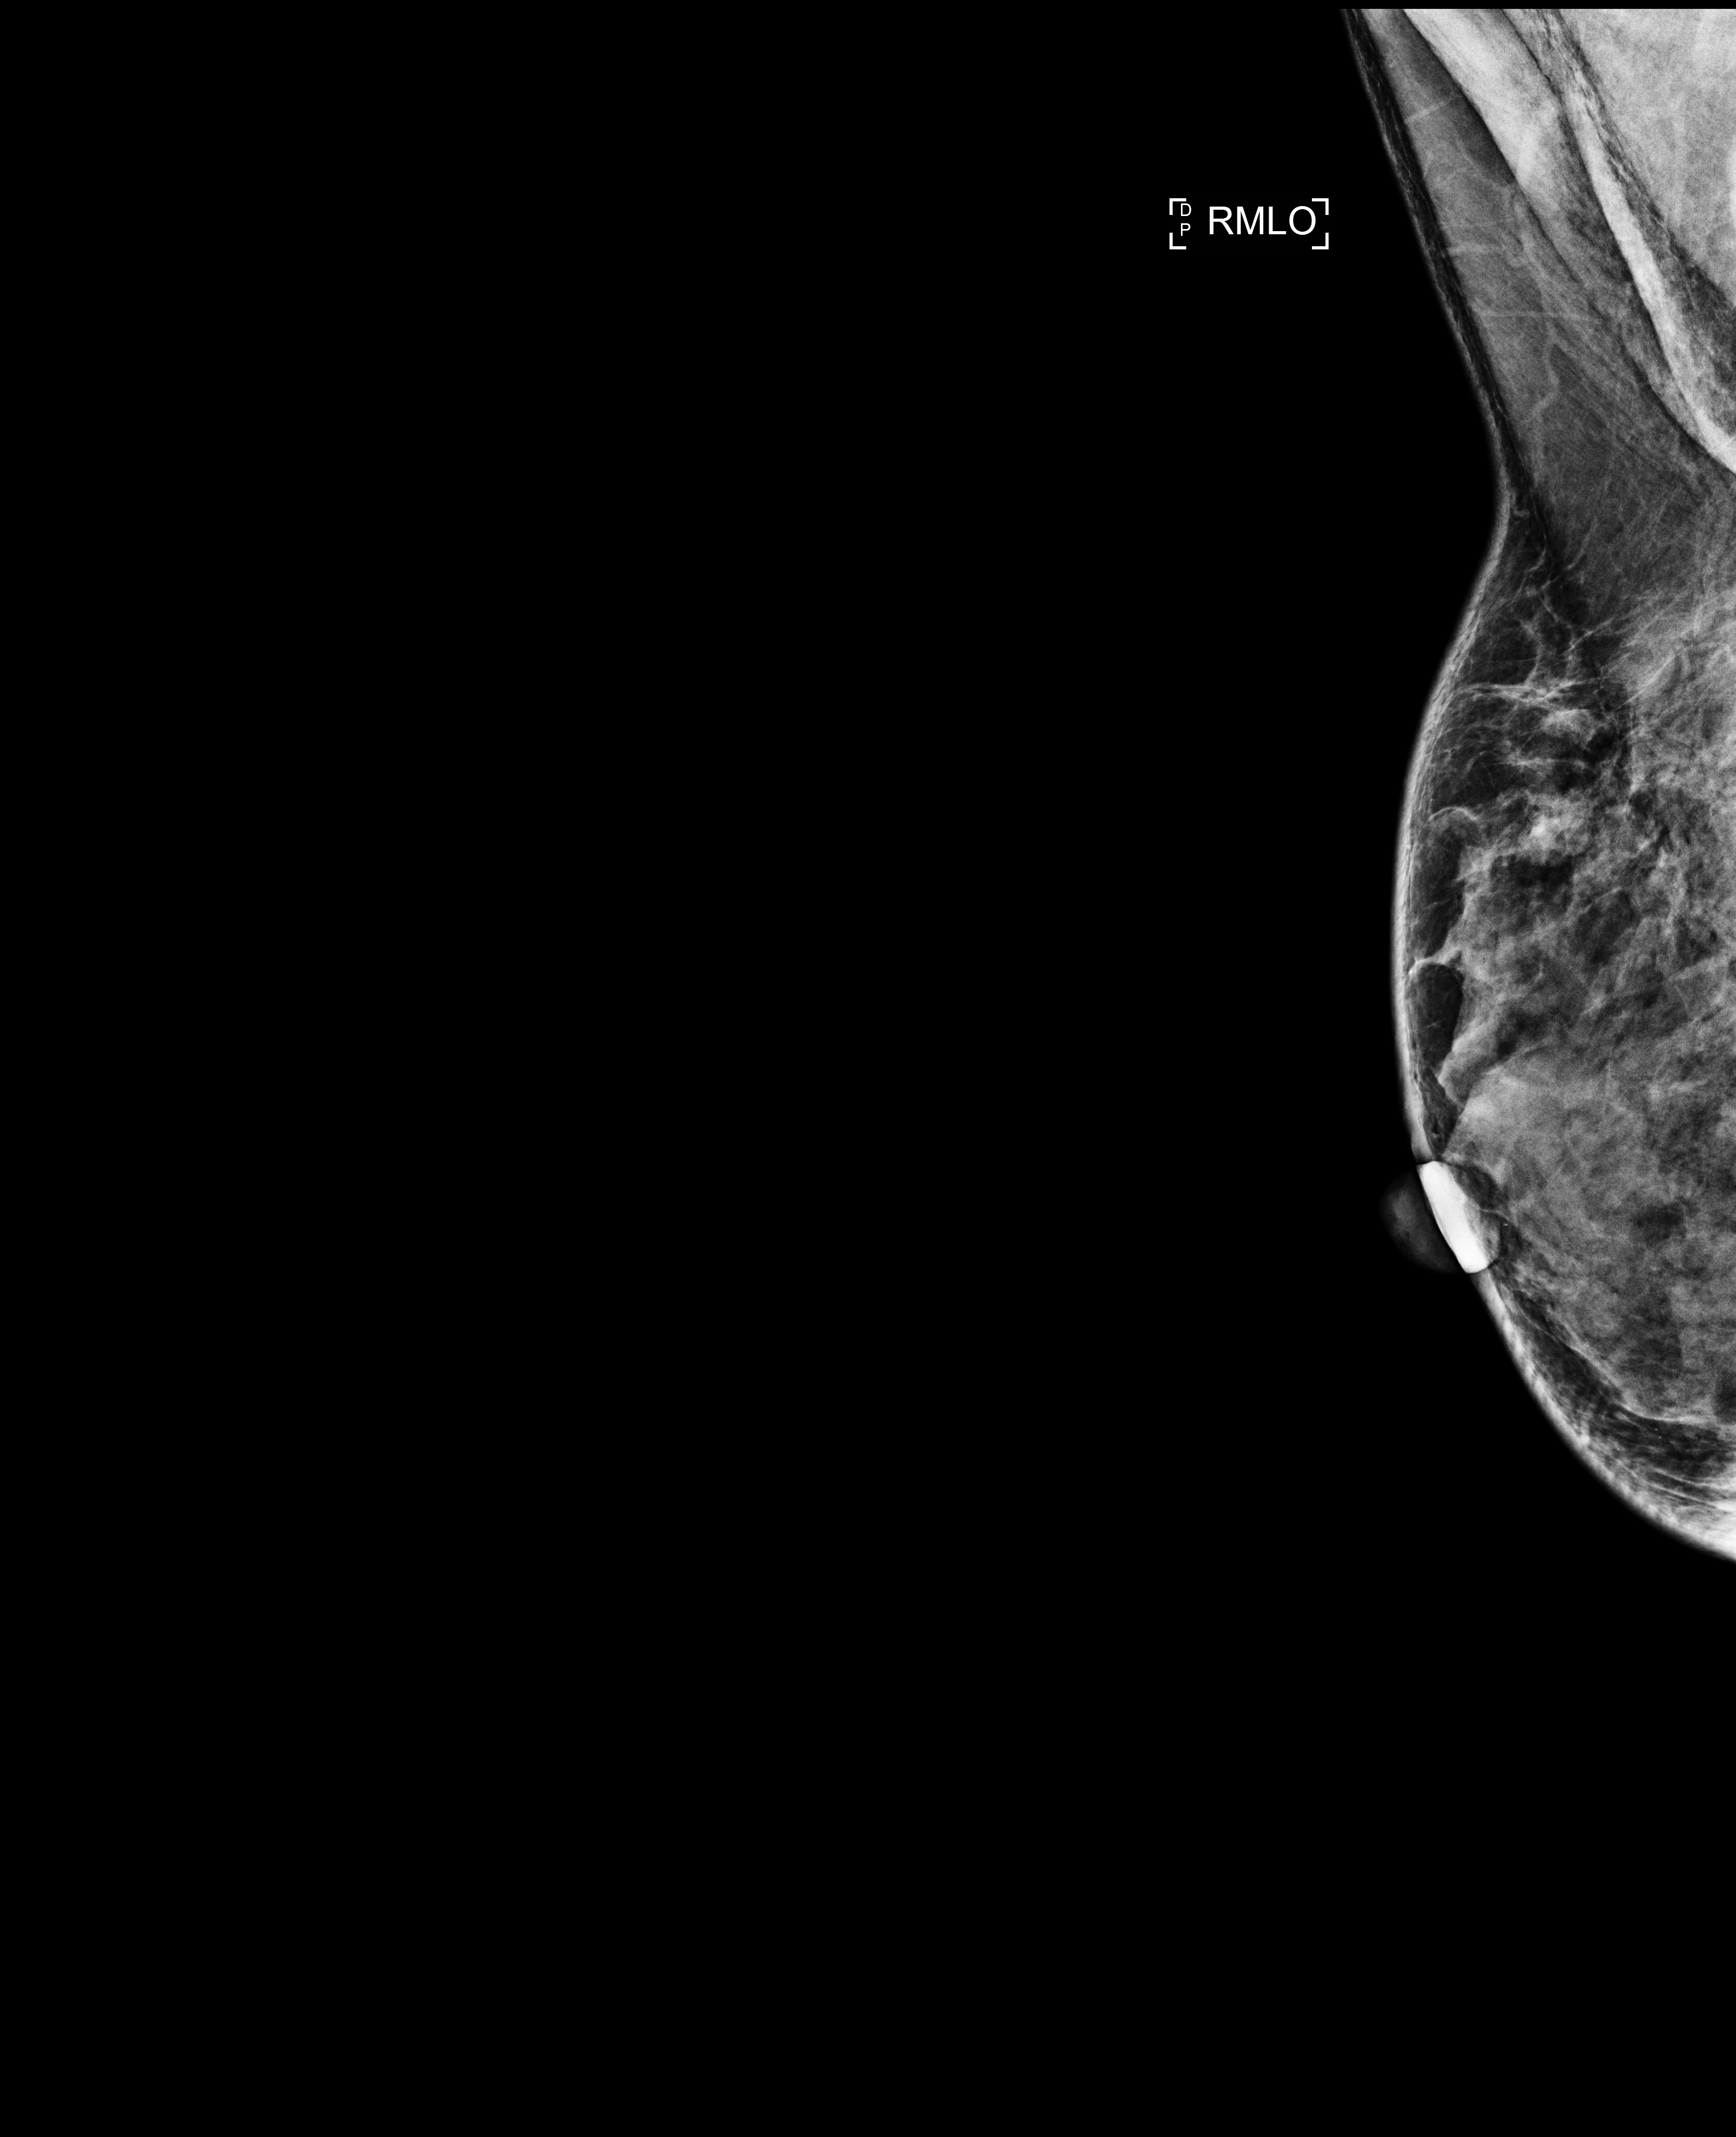
Screening examination. Female patient, age 60 years.
Image type: full-field digital mammogram. Breast: right. Projection: MLO view.